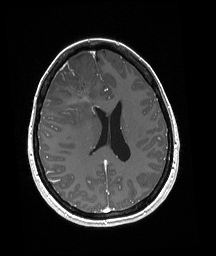
Brain MRI from a brain-tumour surgery series, one axial slice. Position 80 of 192 along the scan axis. T1-weighted post-contrast. 1 mm slice thickness. 216 × 256 image matrix, field of view 211 × 250 mm. Case-level facts recorded for this patient, not image findings: histopathology: Oligodendroglioma; WHO grade: 3; IDH mutation: yes.
Structures marked on this image (outlined manually by an expert reader):
- tumour: bounding box (x1, y1, x2, y2) in pixels: (57, 81, 94, 101)